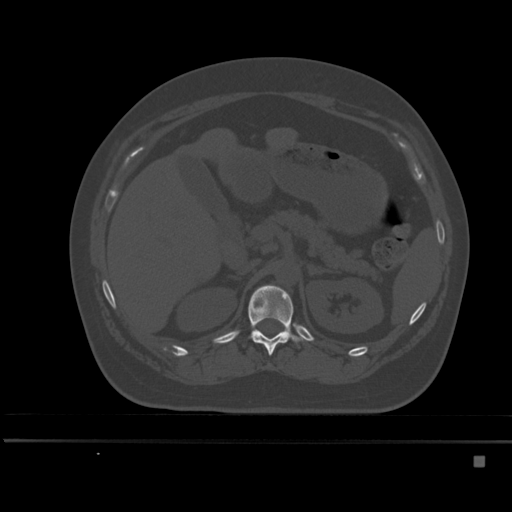
CT including the spine, one axial slice; slice 212 of 495 in the series (ordered by position); bone window (W 1800 / L 400 HU); 1.5 mm slice thickness; 512 × 512 image matrix, field of view 404 × 404 mm. Female patient, age 33 years. From the clinical record (not read from this slice): primary cancer: breast; vertebrae with lytic lesions (as recorded): T1.
Structures marked on this image (semi-automatic segmentation, software-assisted and operator-edited):
- T12 vertebra: bounding box (x1, y1, x2, y2) in pixels: (248, 285, 305, 355)